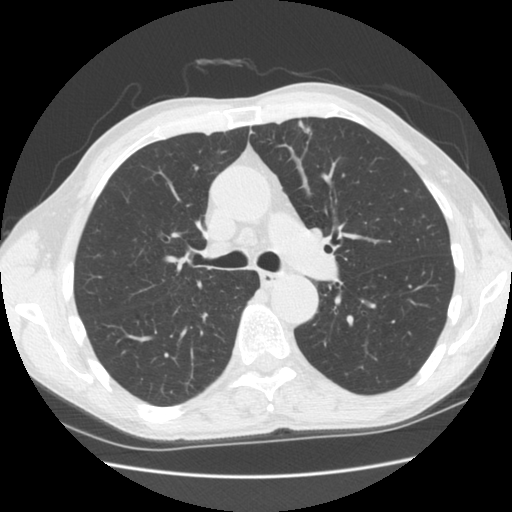
Low-dose screening chest CT, one axial slice. Lung window (W 1500 / L -600 HU). 2.5 mm slice thickness. 512 × 512 image matrix, field of view 340 × 340 mm.
Outlined on this slice (manually delineated by an expert):
- lesion 1 (tumor, upper lobe of left lung): bounding box (x1, y1, x2, y2) in pixels: (298, 120, 311, 134)